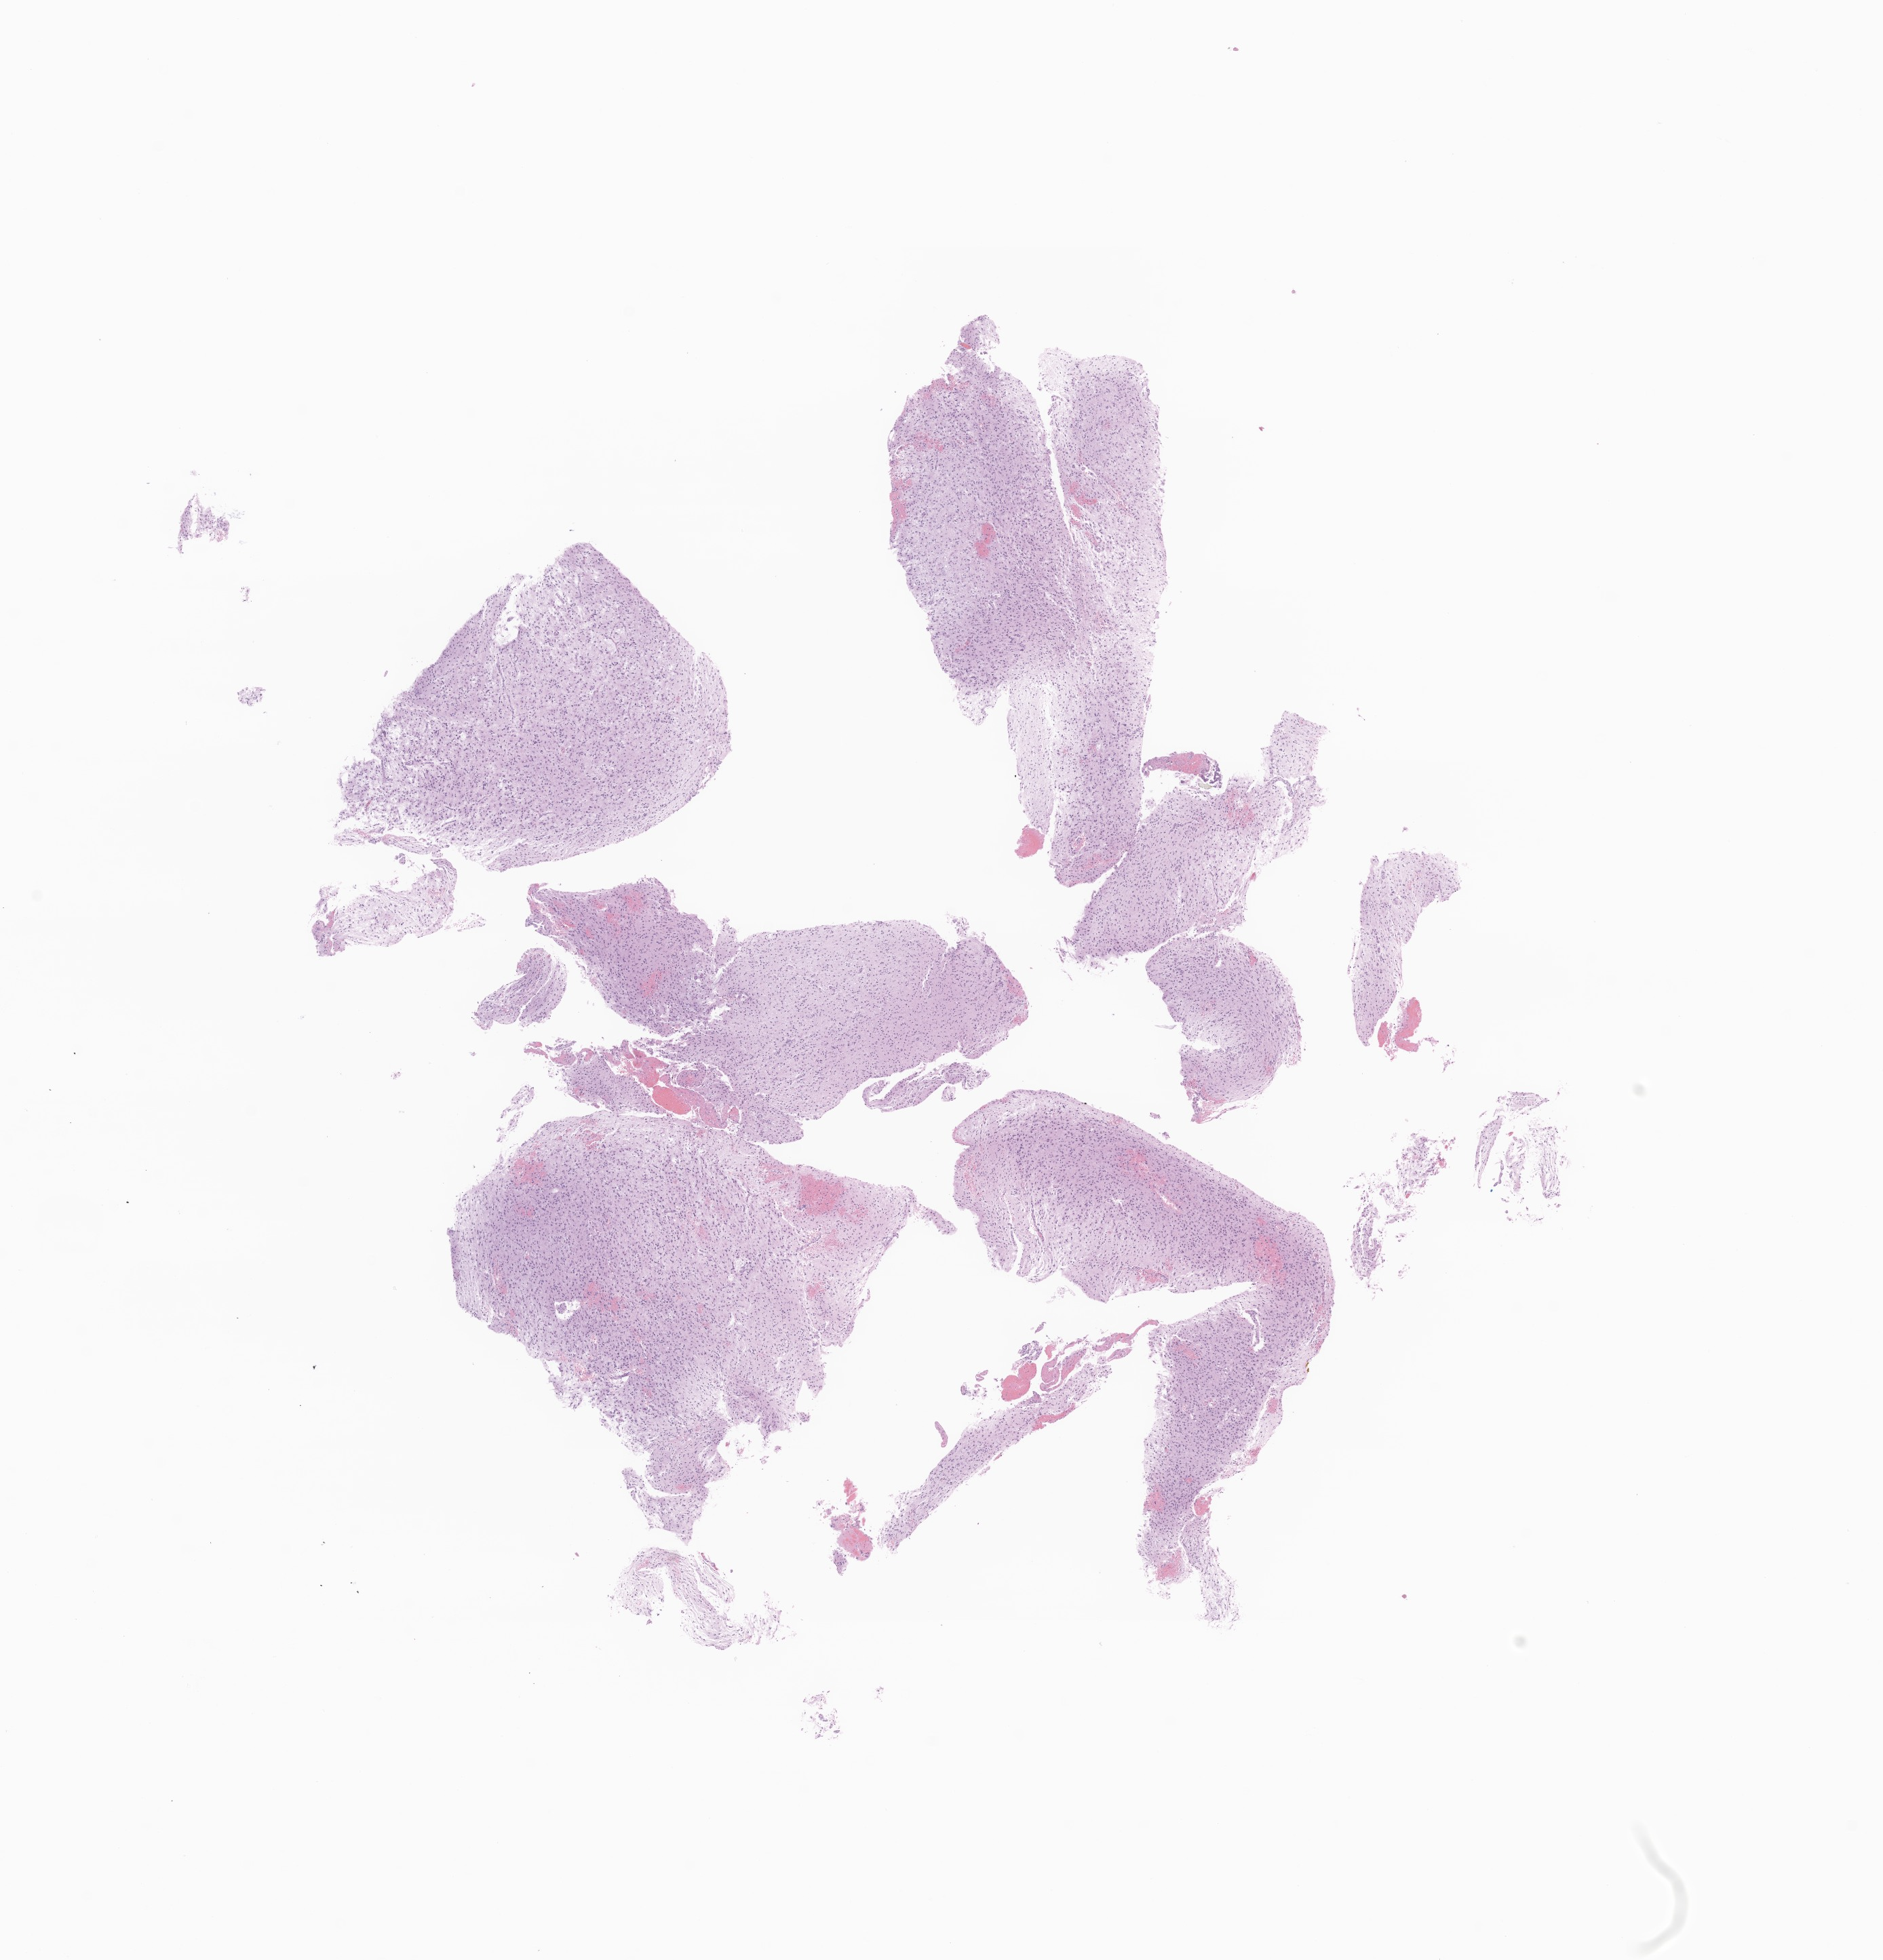
Whole-slide image, haematoxylin and eosin stain of tumor tissue from the brain — whole scanned area (about 11.7 x 12.2 mm) shown as a low-resolution overview. FFPE section. Female patient, age 114 months (9 years 6 months).
Diagnosis (ICD-O-3 morphology term): Glioma, malignant.